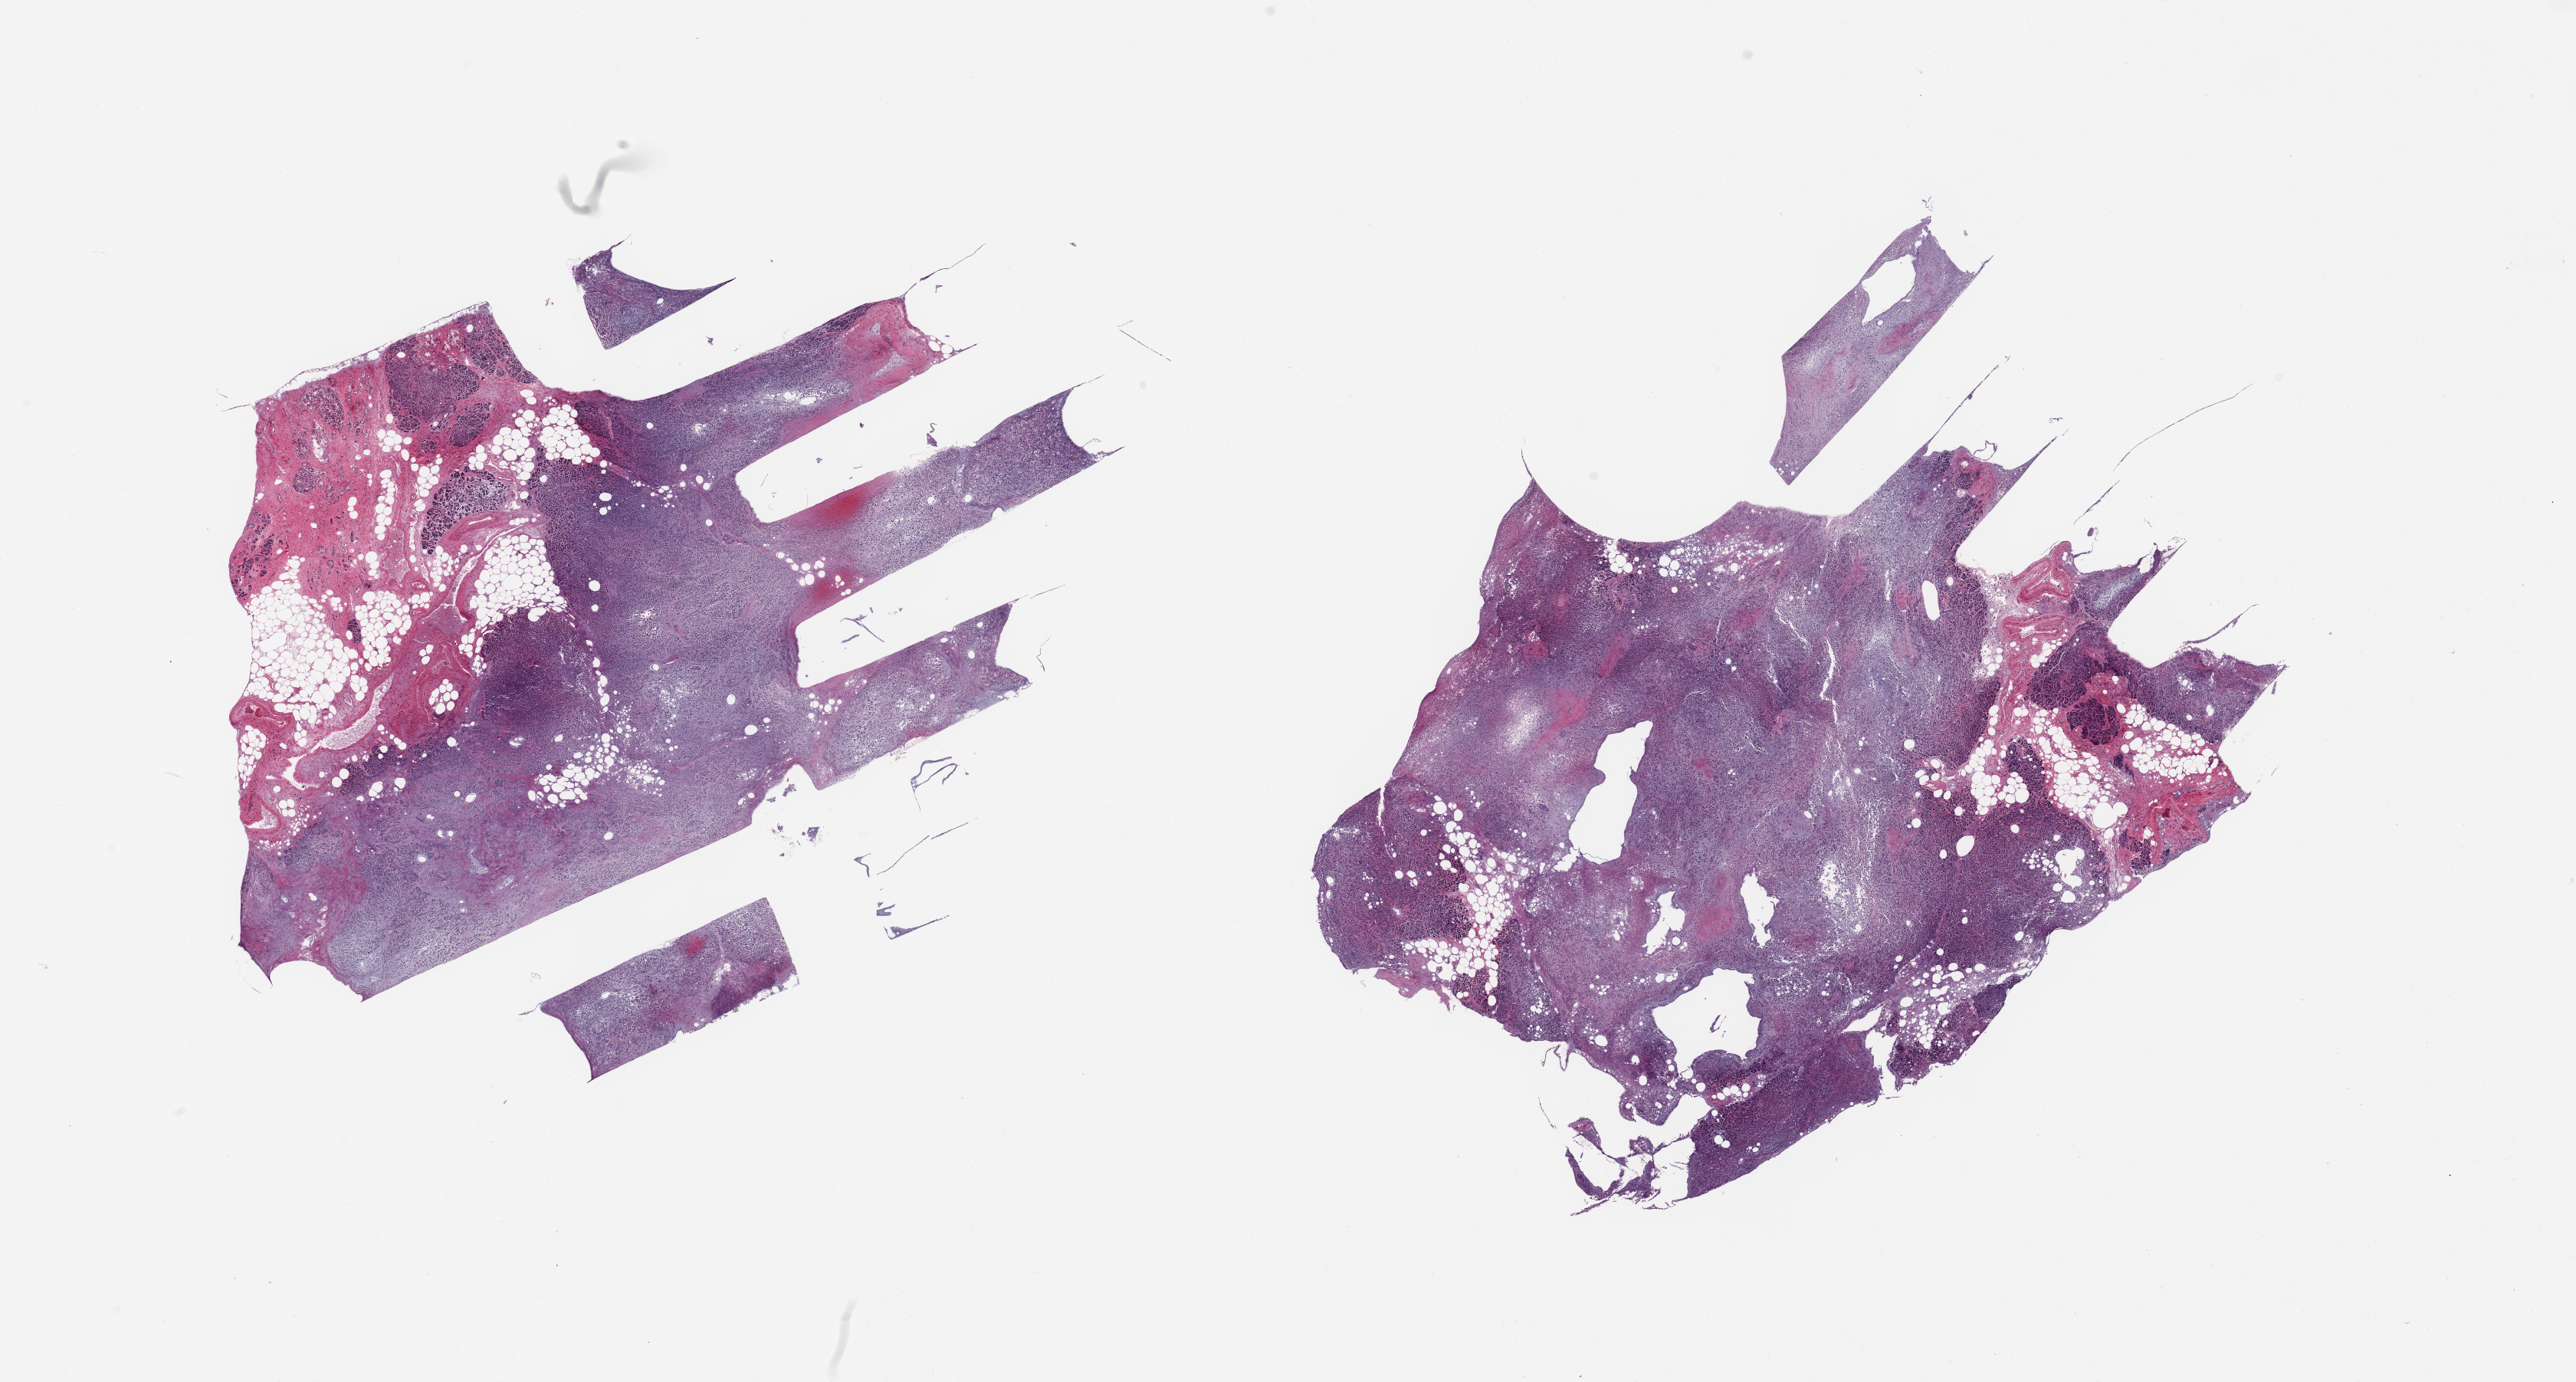
Haematoxylin and eosin whole-slide image, shown as a low-resolution overview of the whole scanned area (about 26.6 x 14.3 mm); PAXgene-fixed, paraffin-embedded tissue; sampled site (target tissue): pancreas; donor tissue sample. Donor: male.
- review note (as recorded): 2 pieces; large areas of complete autolysis